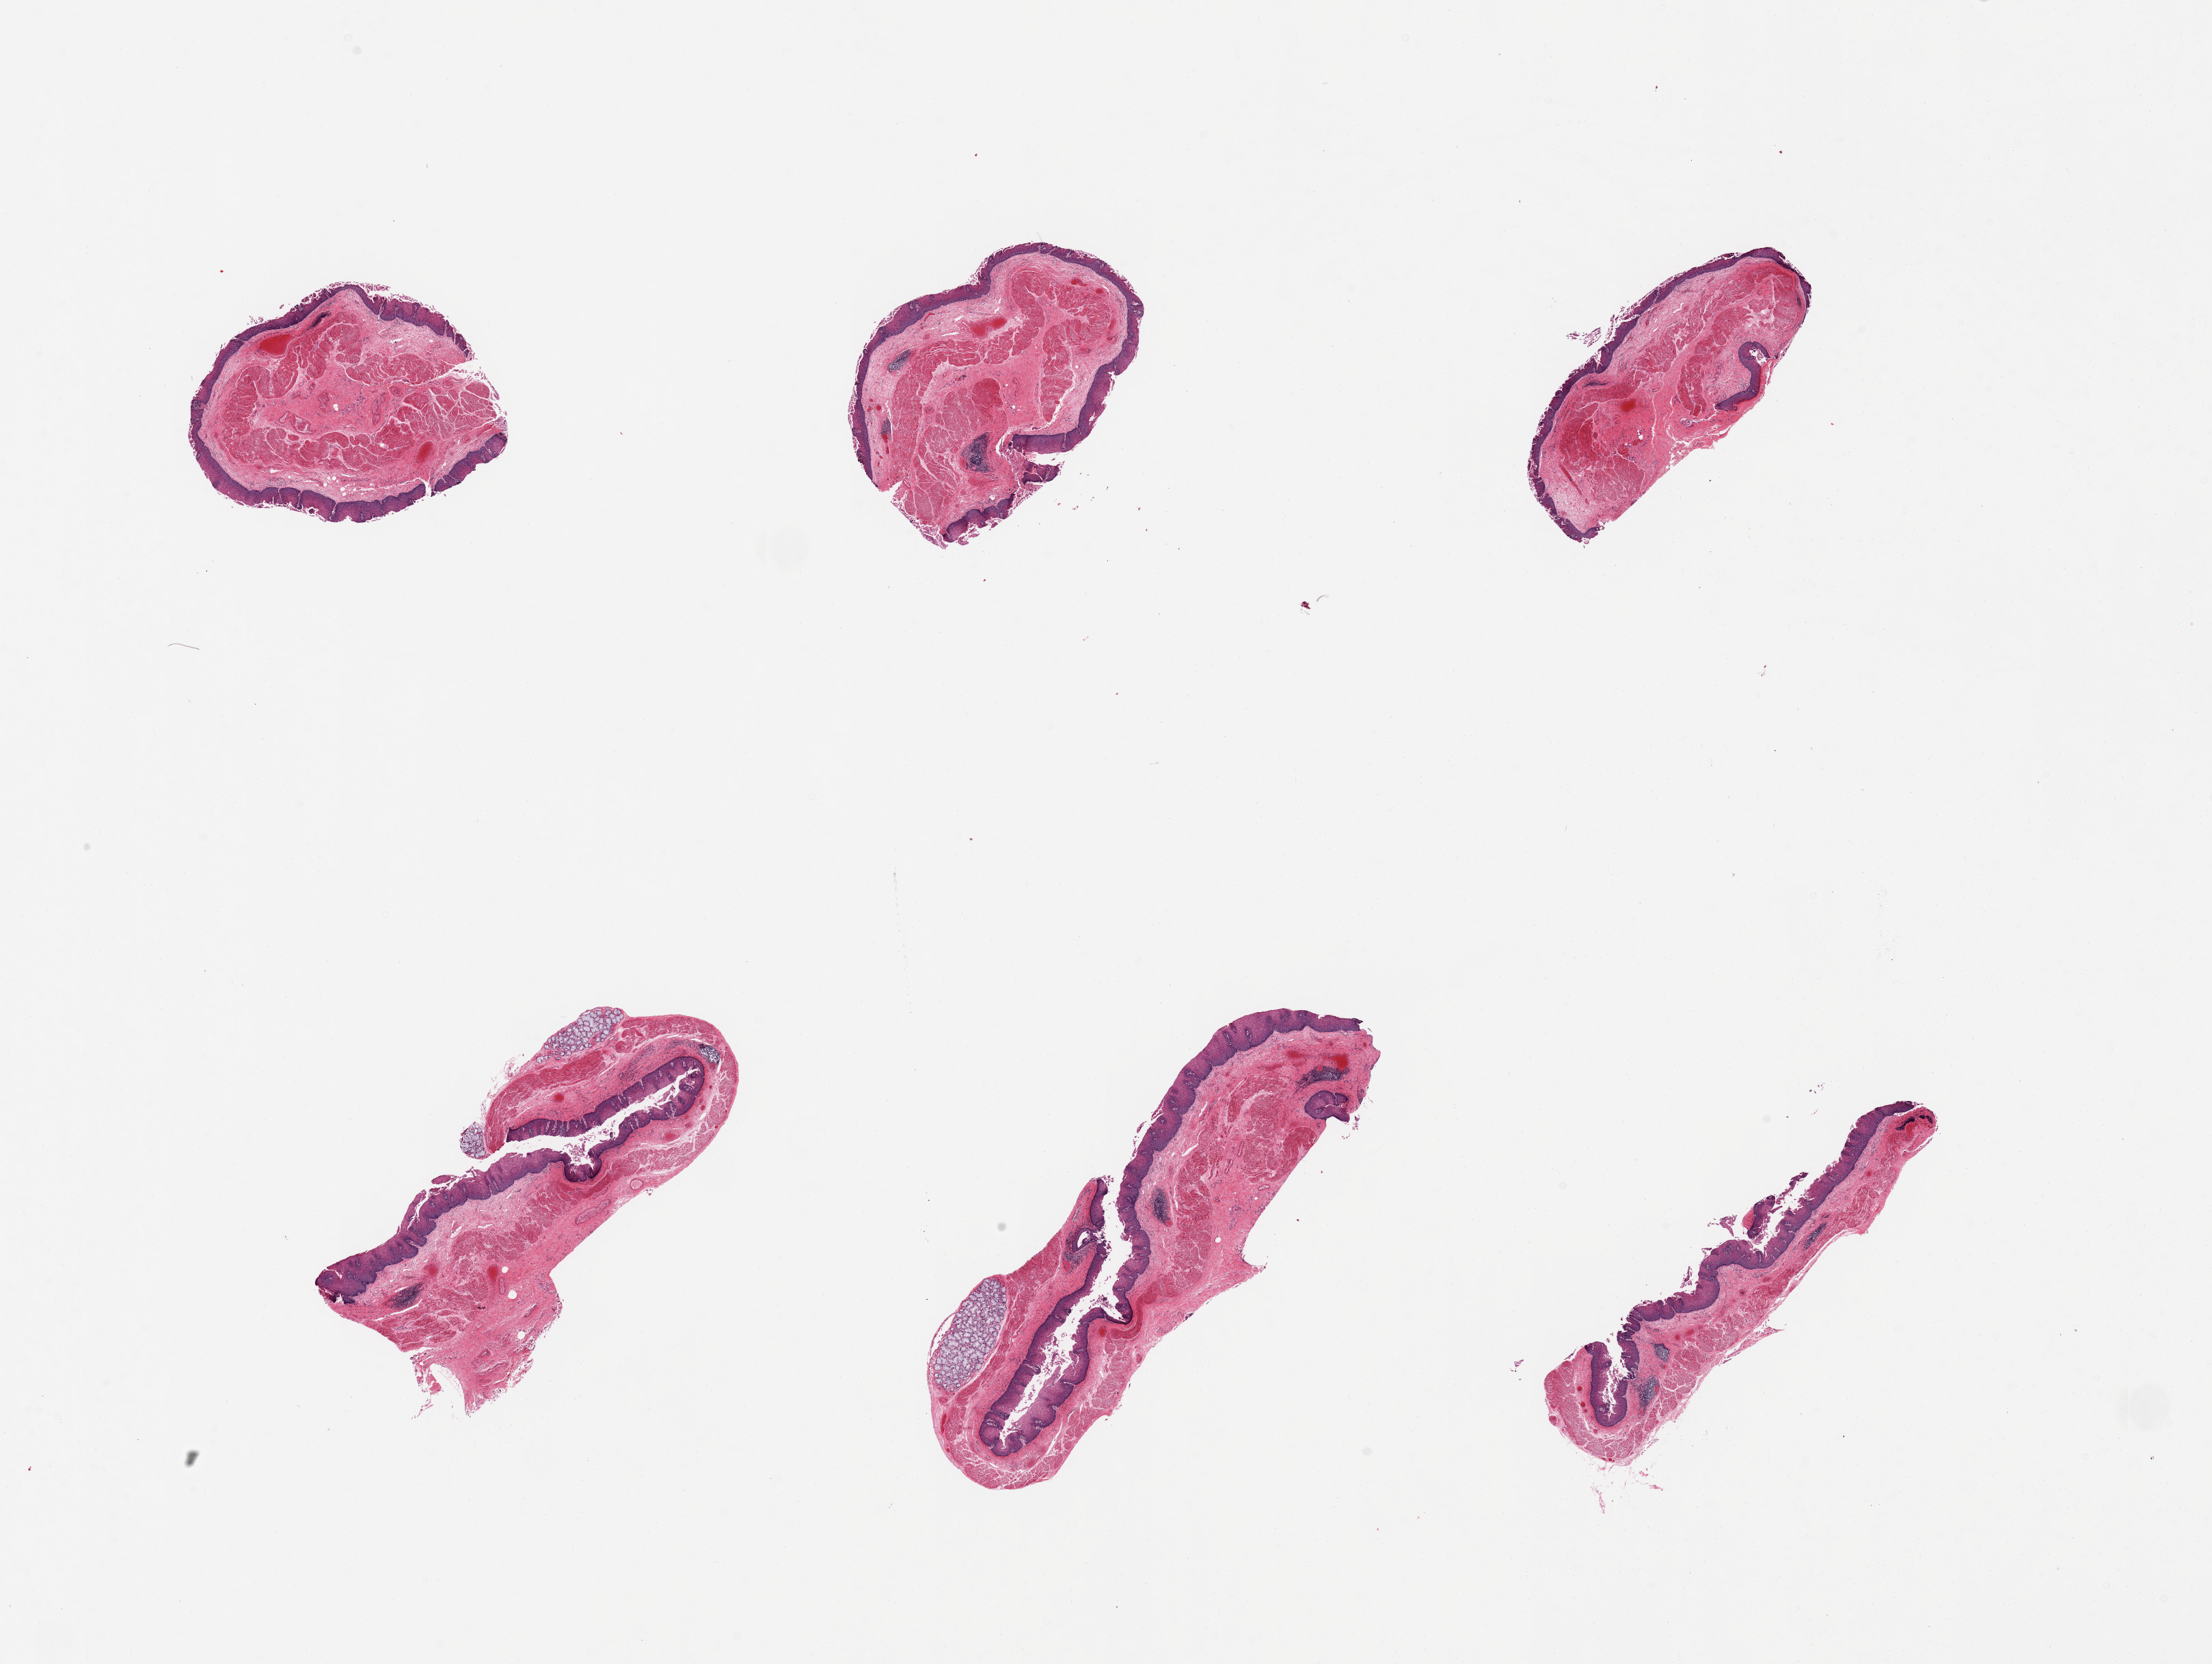
Haematoxylin and eosin whole-slide image — low-resolution overview of the scanned area, about 25.6 x 19.3 mm (acquisition: 20x scan); PAXgene-fixed, paraffin-embedded tissue; sampled site (target tissue): esophageal mucous membrane; donor tissue sample. Donor: male.
Pathologist's review note for this sample: 6 pieces, epithelium partially sloughing, some submucosal glands.